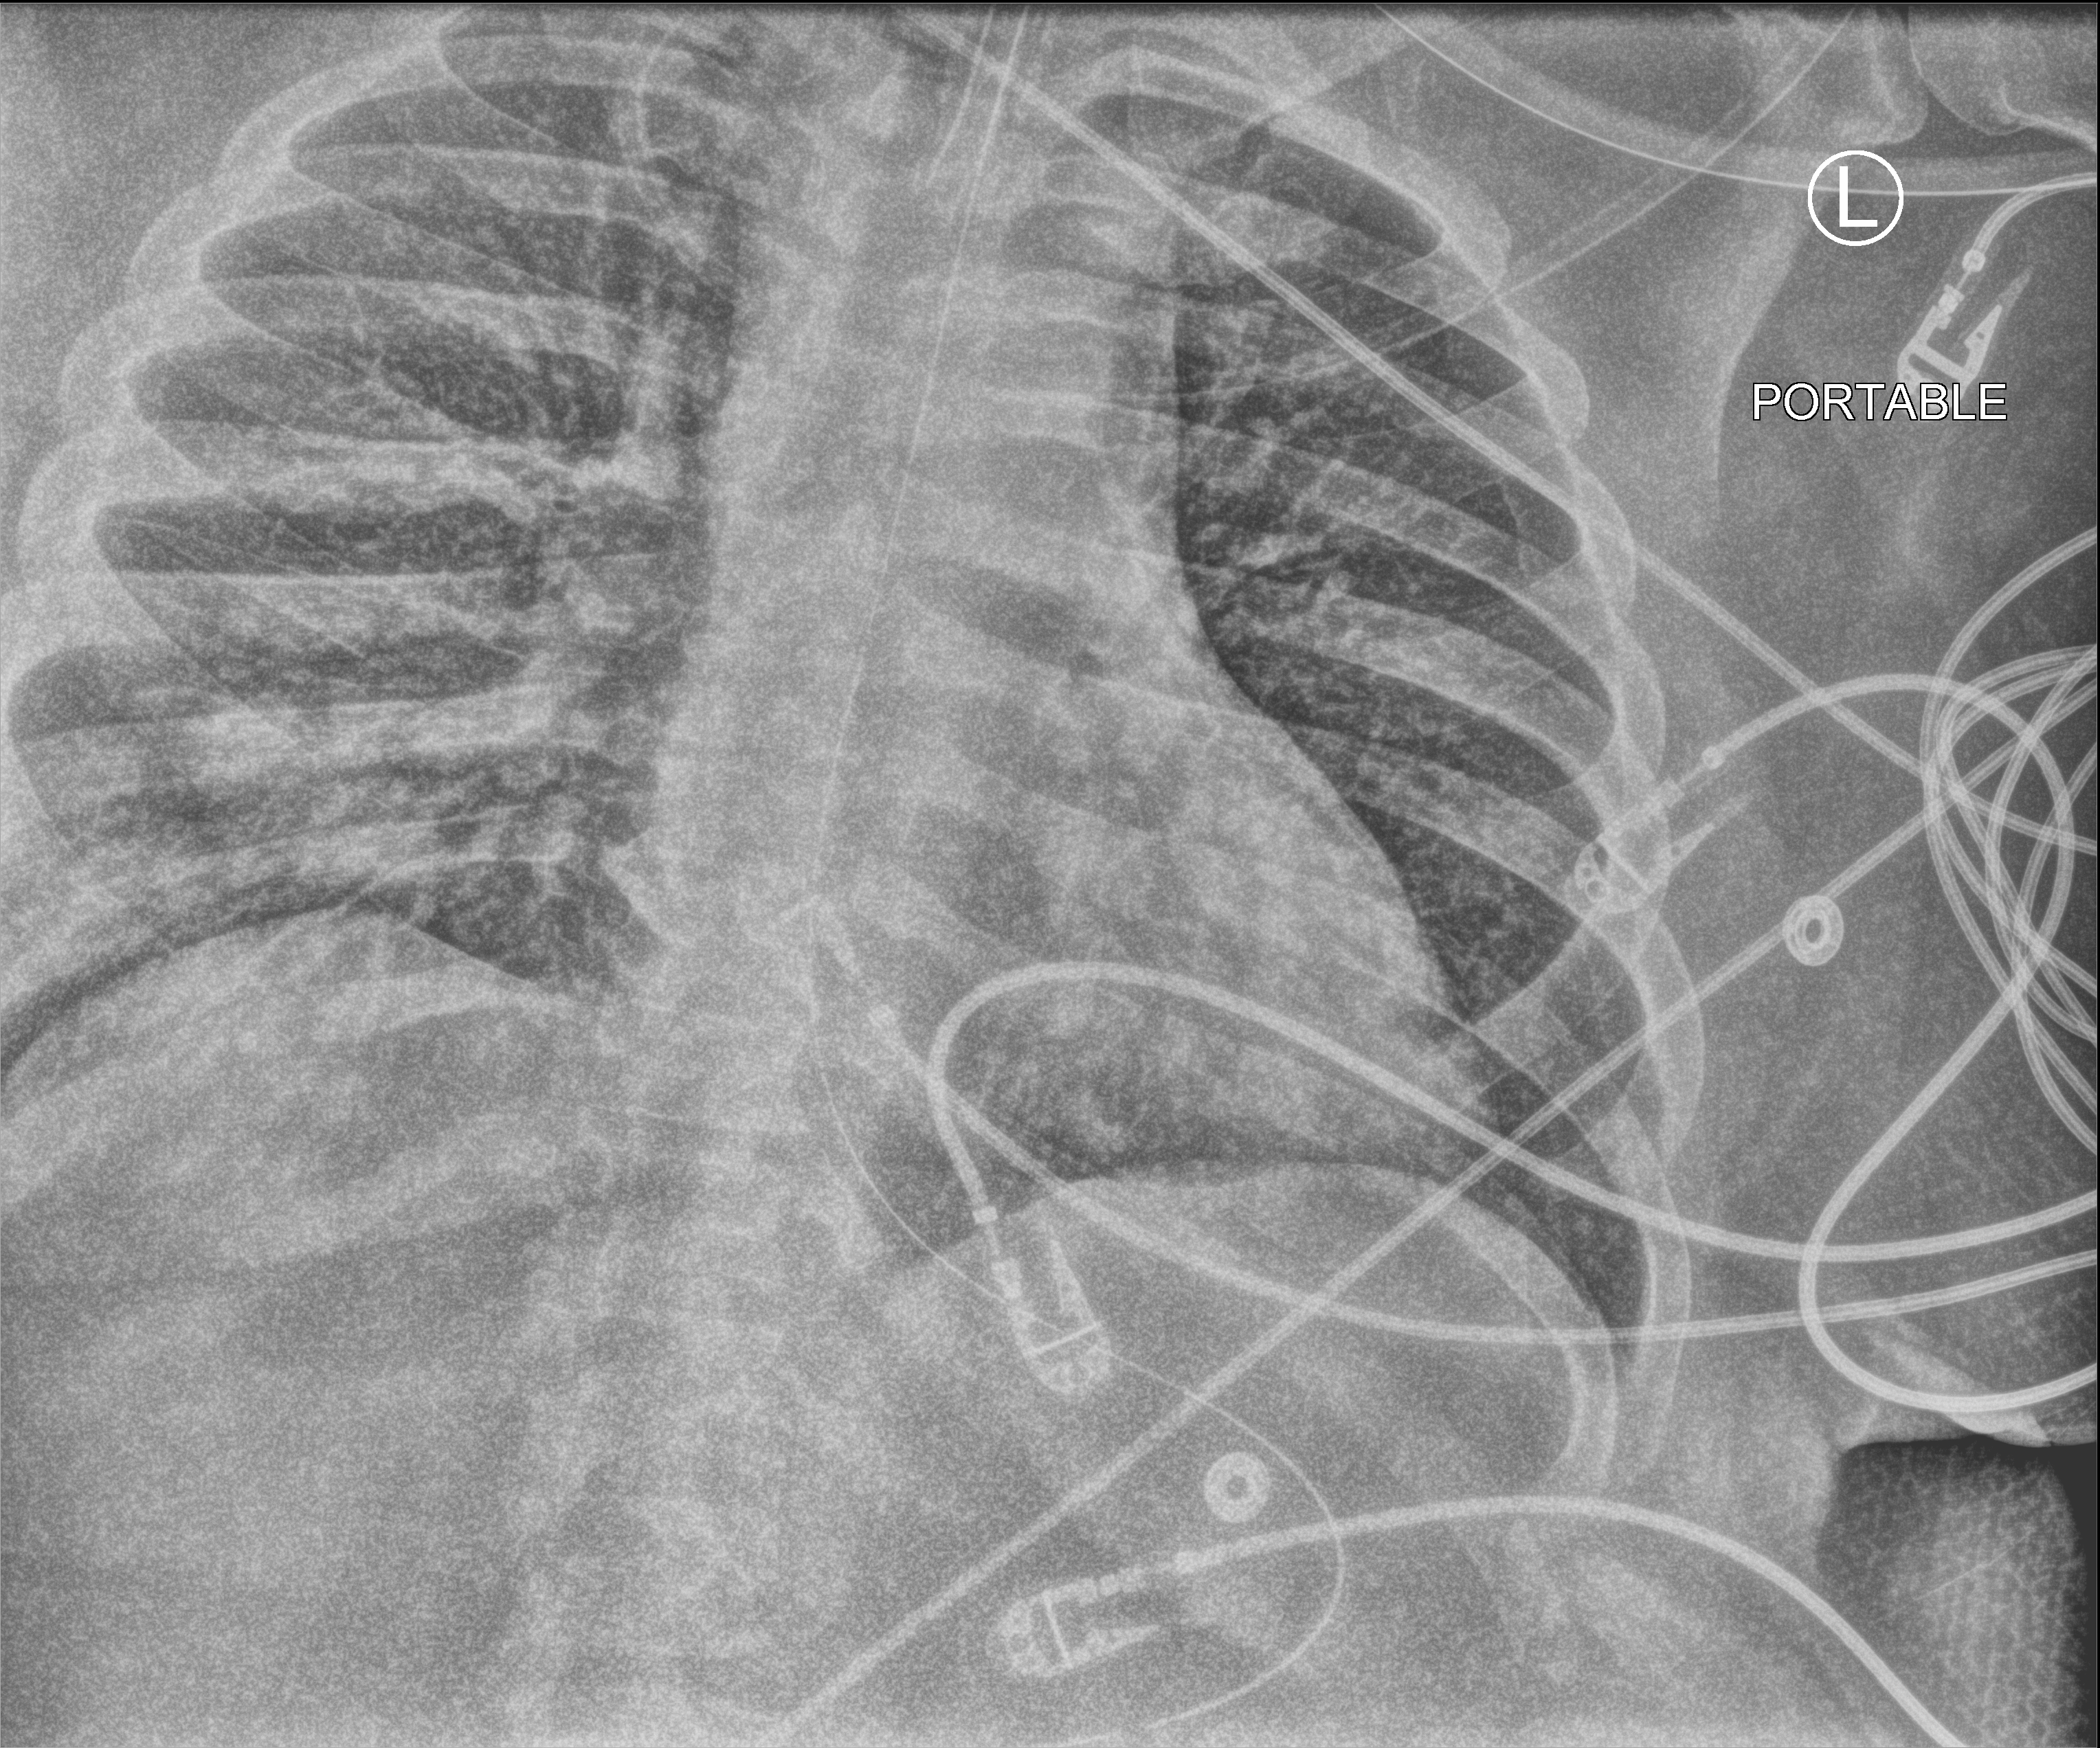
Bedside chest radiograph (computed radiography); anteroposterior (AP) projection. Adult patient hospitalised with COVID-19, age 18–59 years.
From the hospital-stay record, not from the radiograph (when in the stay this image was taken is not recorded): diabetes (admission record): yes; mechanically ventilated during this hospital stay: yes; length of hospital stay: 10 days.